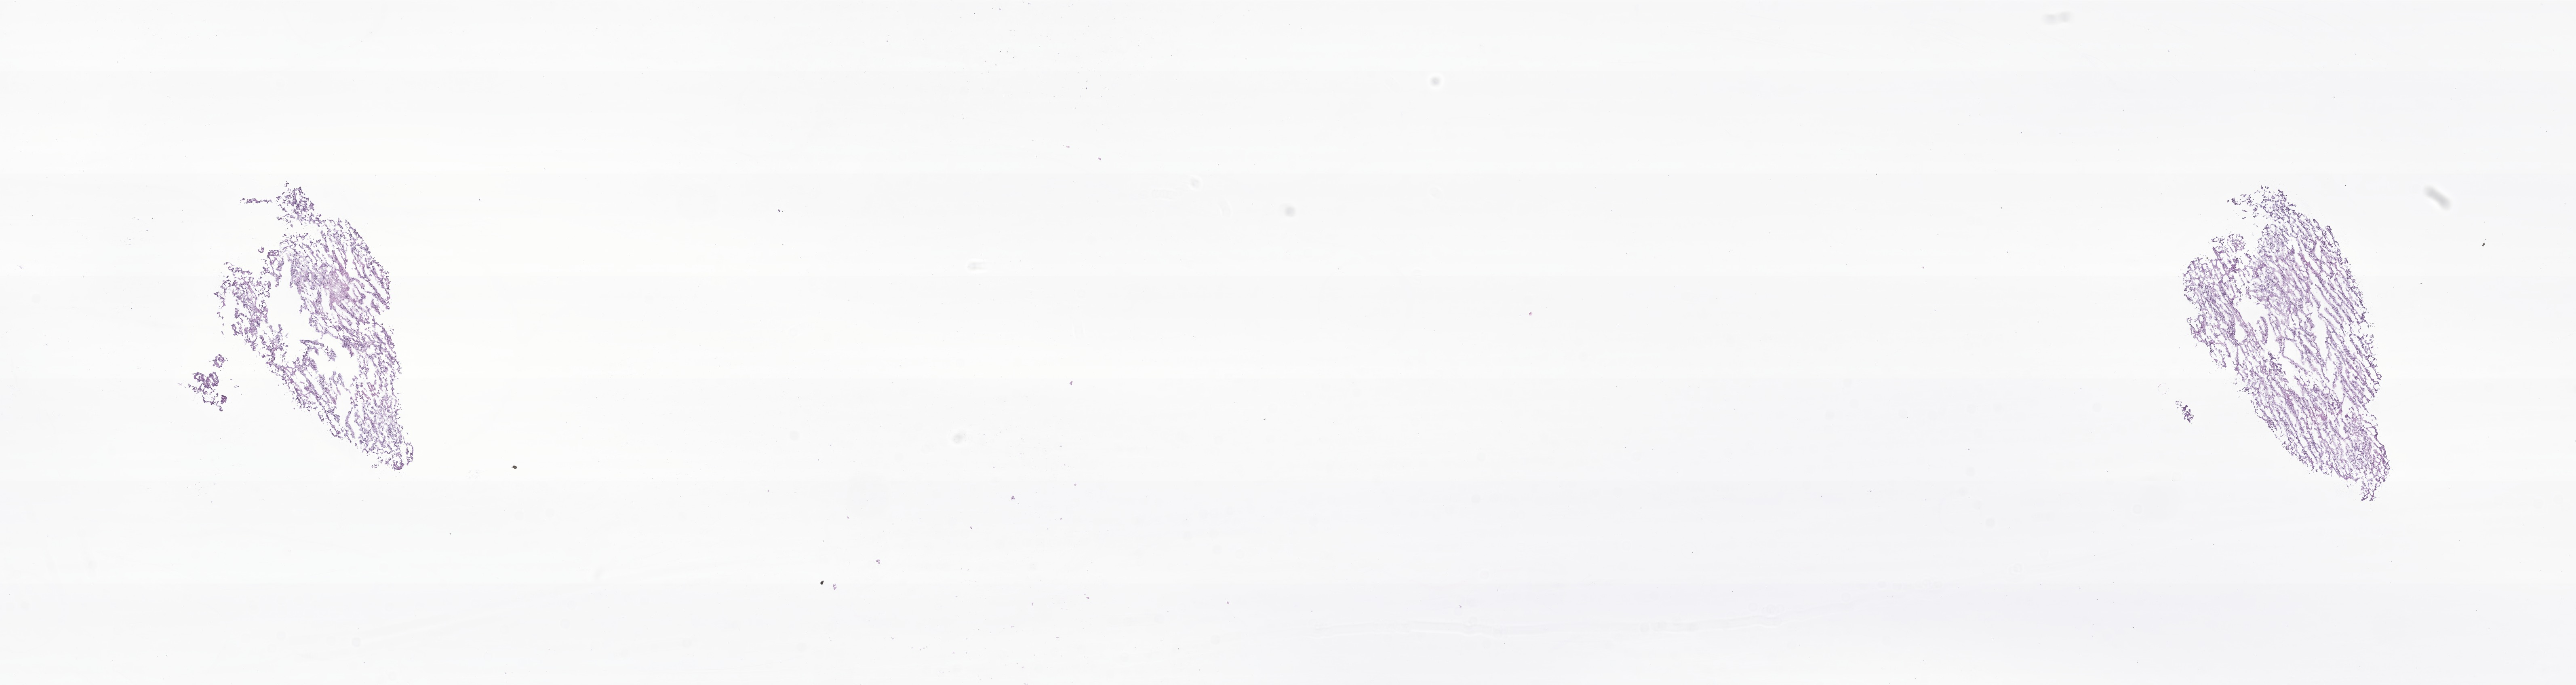
H&E whole-slide image of tumor tissue from the adrenal gland, a low-resolution overview of the entire scanned area, about 26.9 x 7.1 mm. Frozen section. Male patient, age 817 days.
Diagnosis: Neuroblastoma, NOS.